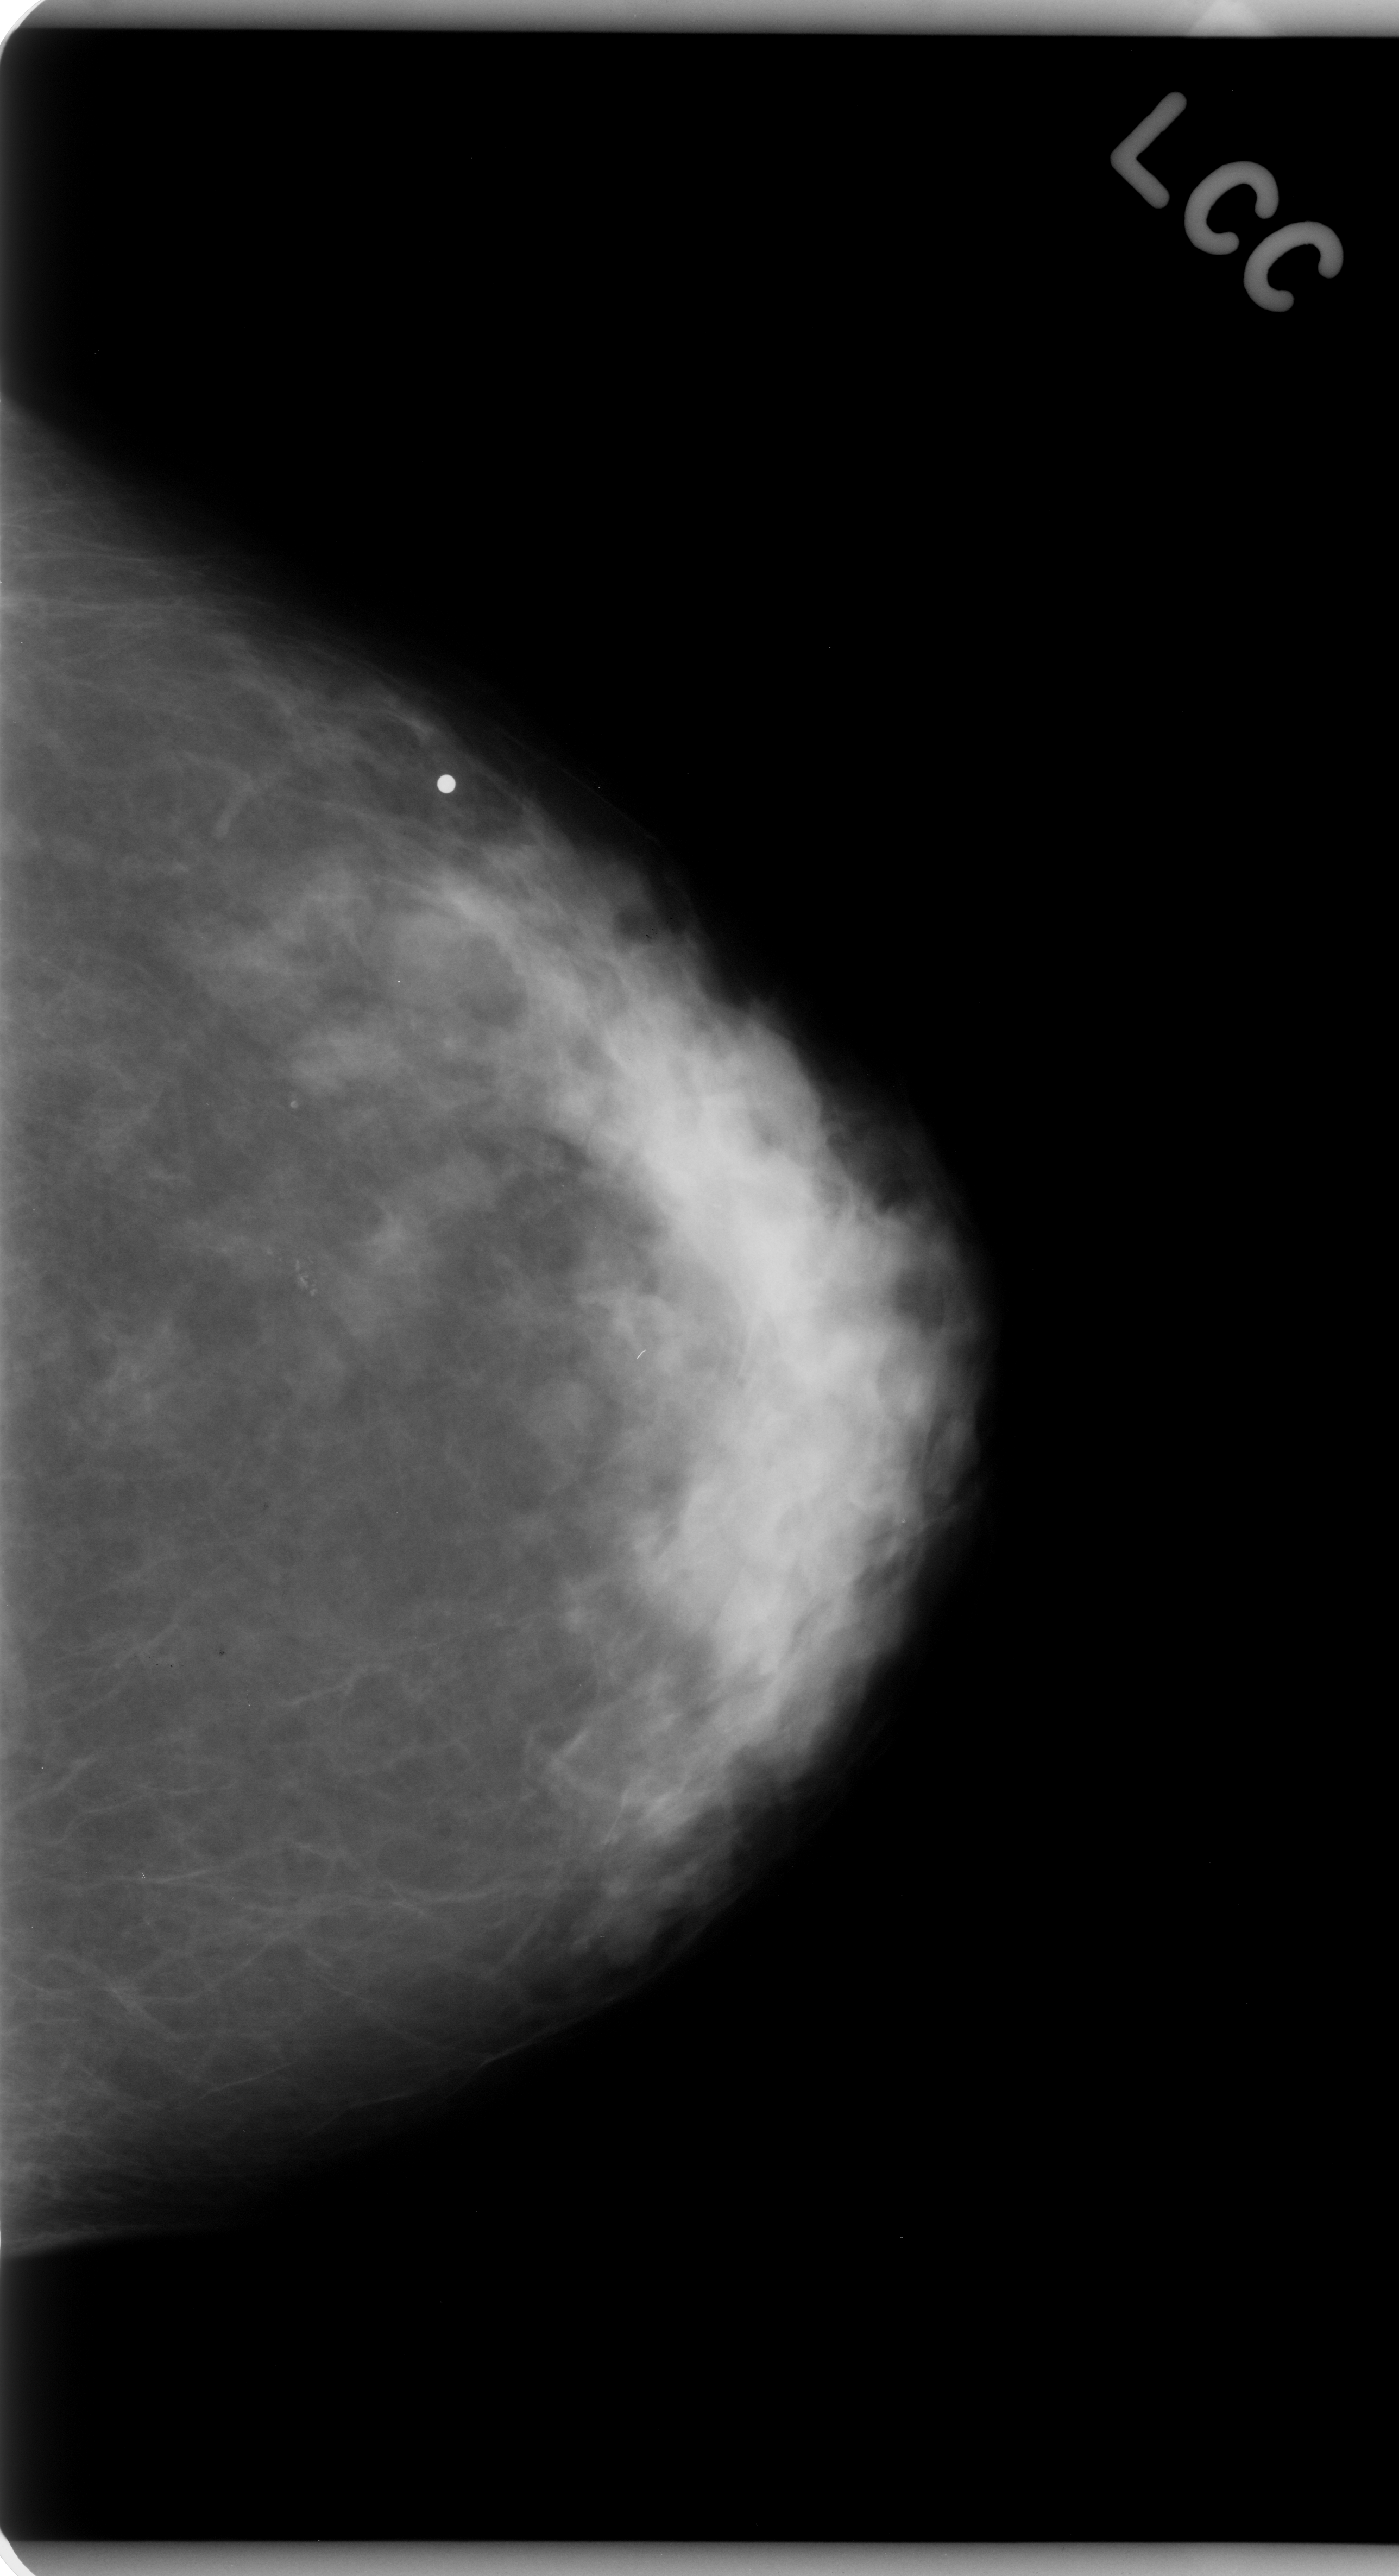
Scanned film-screen mammogram, left breast, craniocaudal (CC) view, breast composition: heterogeneously dense (BI-RADS density category 3 of 4).
- Radiologist-marked abnormalities on this image: mass, shape round, margins circumscribed; BI-RADS assessment category 3; subtlety rating 4 on a 1 (subtle) to 5 (obvious) scale; pathology (as recorded): benign.